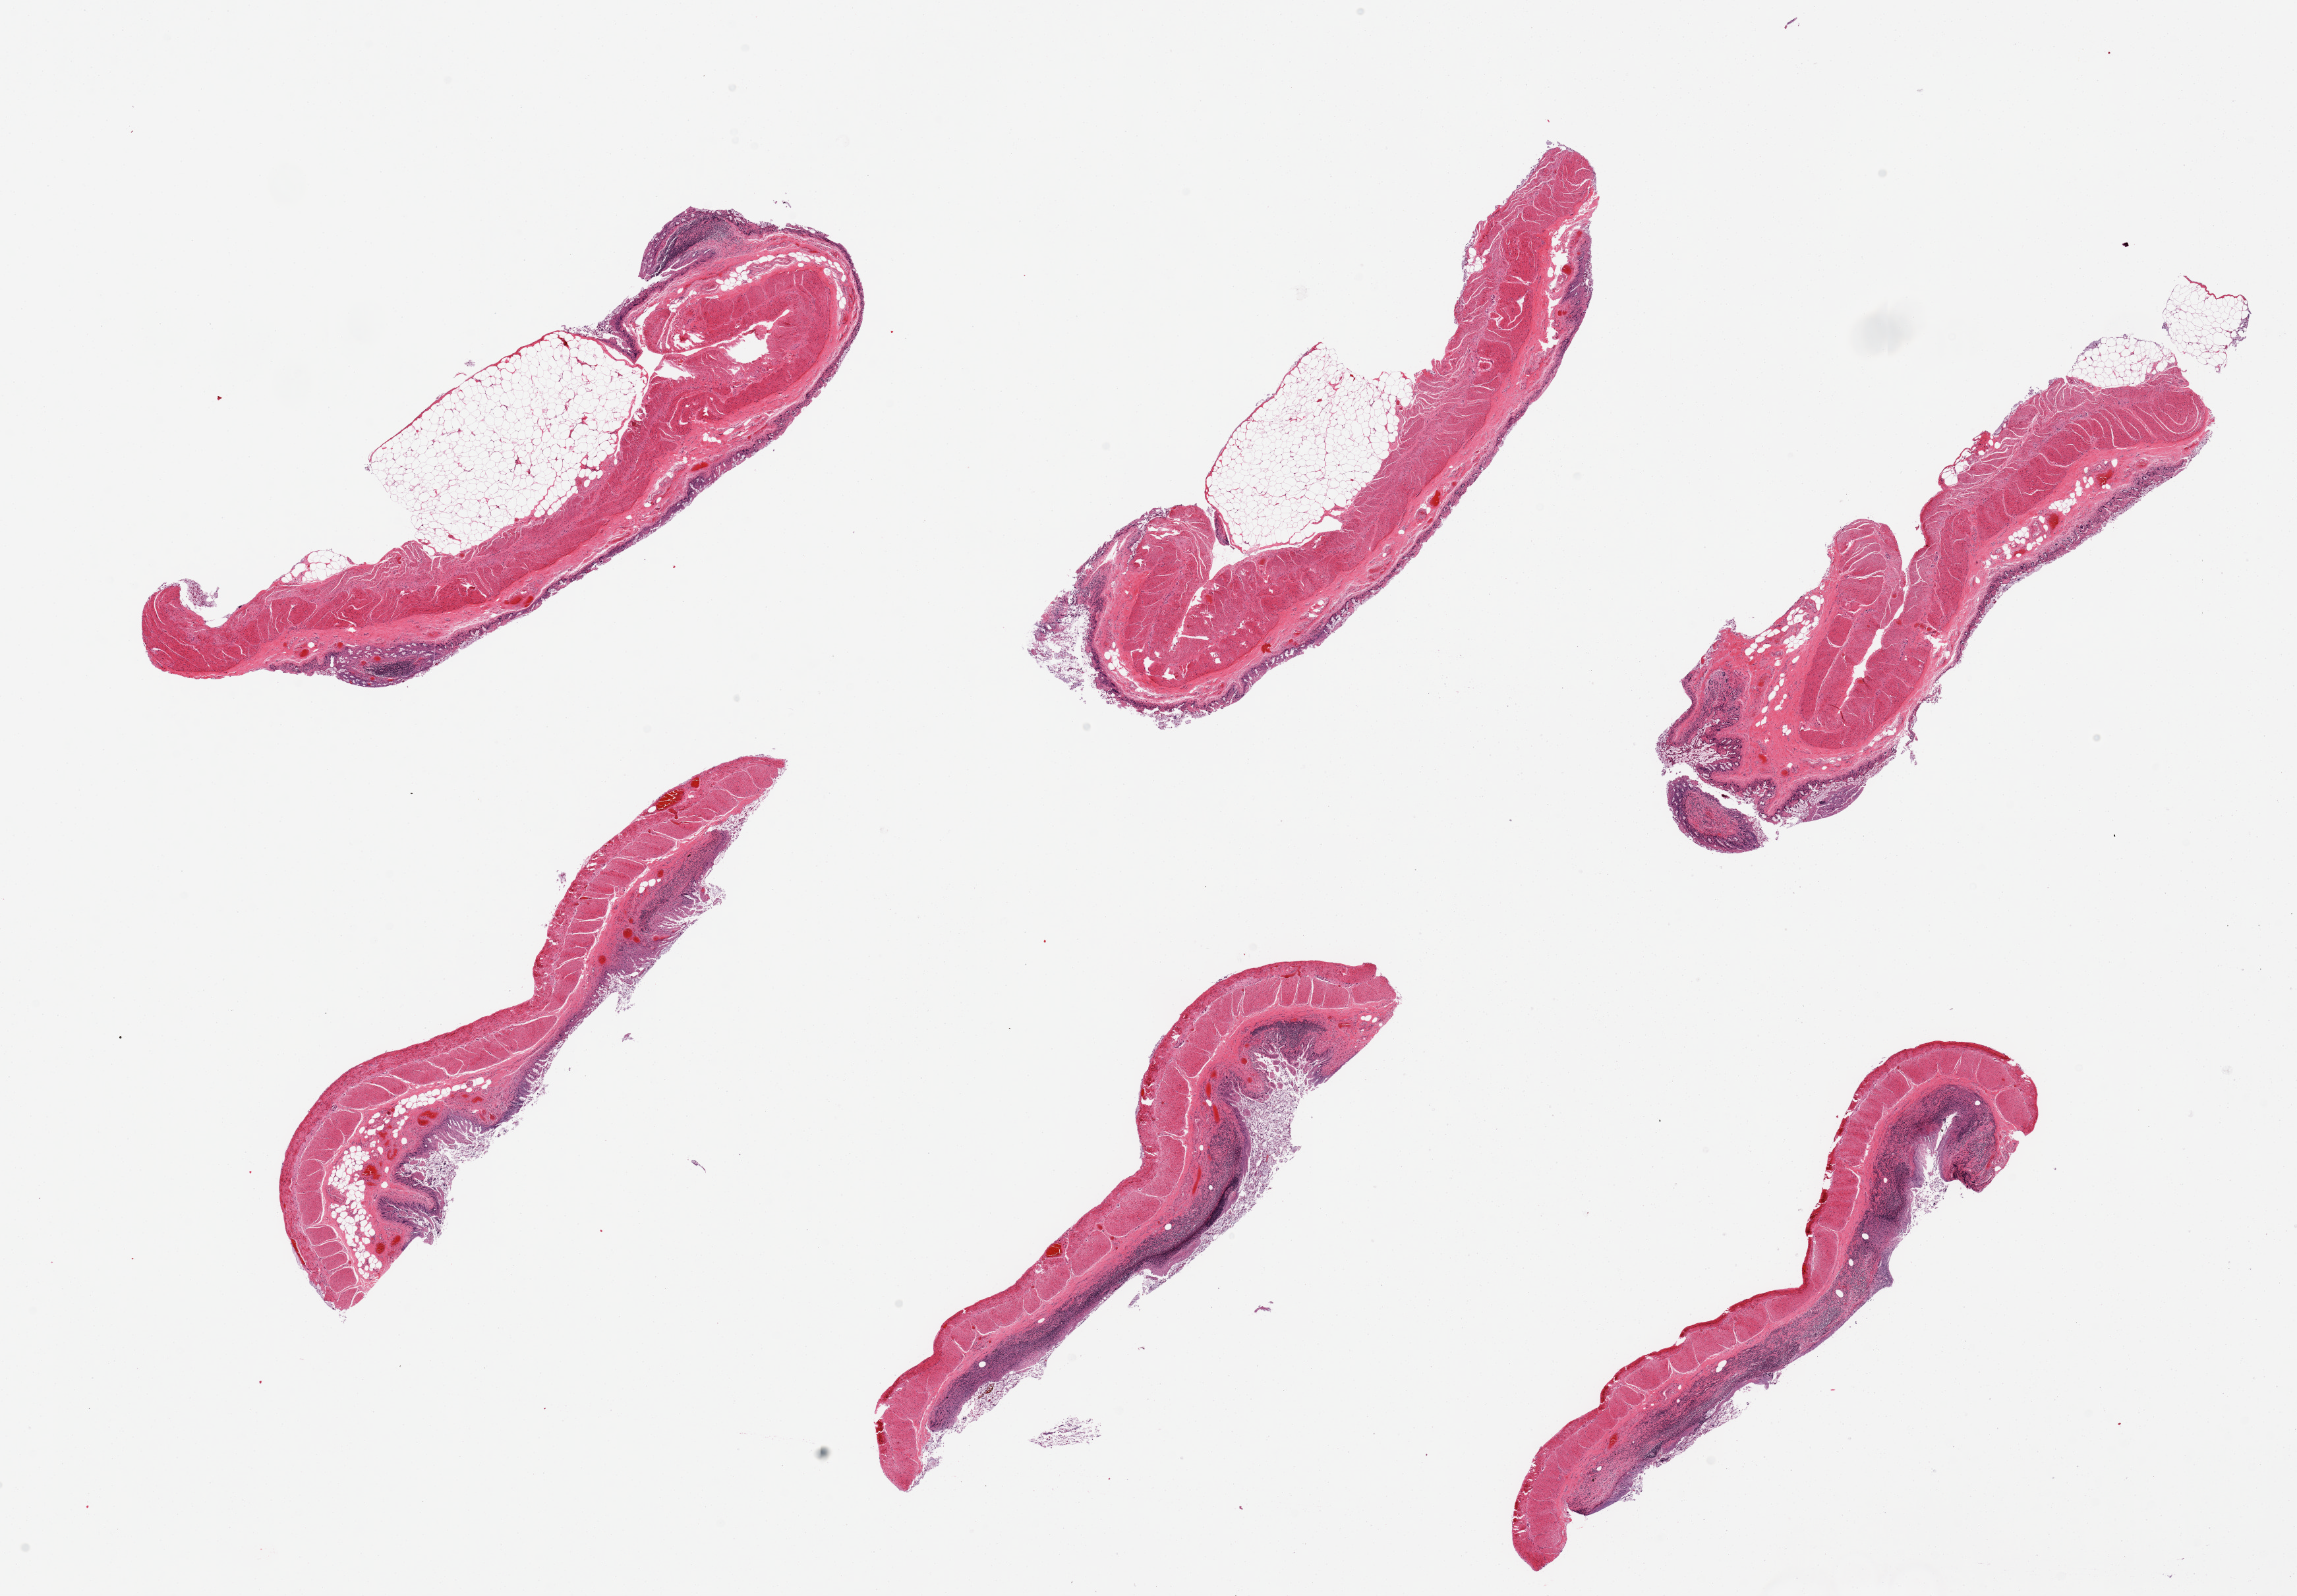
Digitized haematoxylin and eosin-stained section — low-resolution overview of the scanned area, about 27.6 x 19.2 mm (from a 20x scan), PAXgene-fixed paraffin-embedded (PFPE) section, section of ileum (target tissue), donor tissue sample. Donor sex: male.
* reviewer comment on this tissue sample: 6 pieces, muscularis, severely autolyzed mucosa and lymphoid component